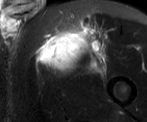
MRI of an extremity soft-tissue mass, one axial slice; slice 50 of 52 in the series (ordered by position); T2-weighted fat-saturated; MR volume resampled by the dataset authors to the PET/CT grid (not the native acquisition matrix); 147 × 122 image matrix, field of view 144 × 119 mm. Male patient. From the clinical record (not read from this slice): histological type: pleiomorphic liposarcoma; grade: high; site of the primary tumour: left thigh.
Structures marked on this image (expert contour drawn on MRI and transferred to this co-registered scan by the dataset authors):
- gross tumour volume including surrounding oedema: bounding box <39,27,104,72> (left, top, right, bottom; pixels)
- gross tumour volume (mass): <39,32,81,63>